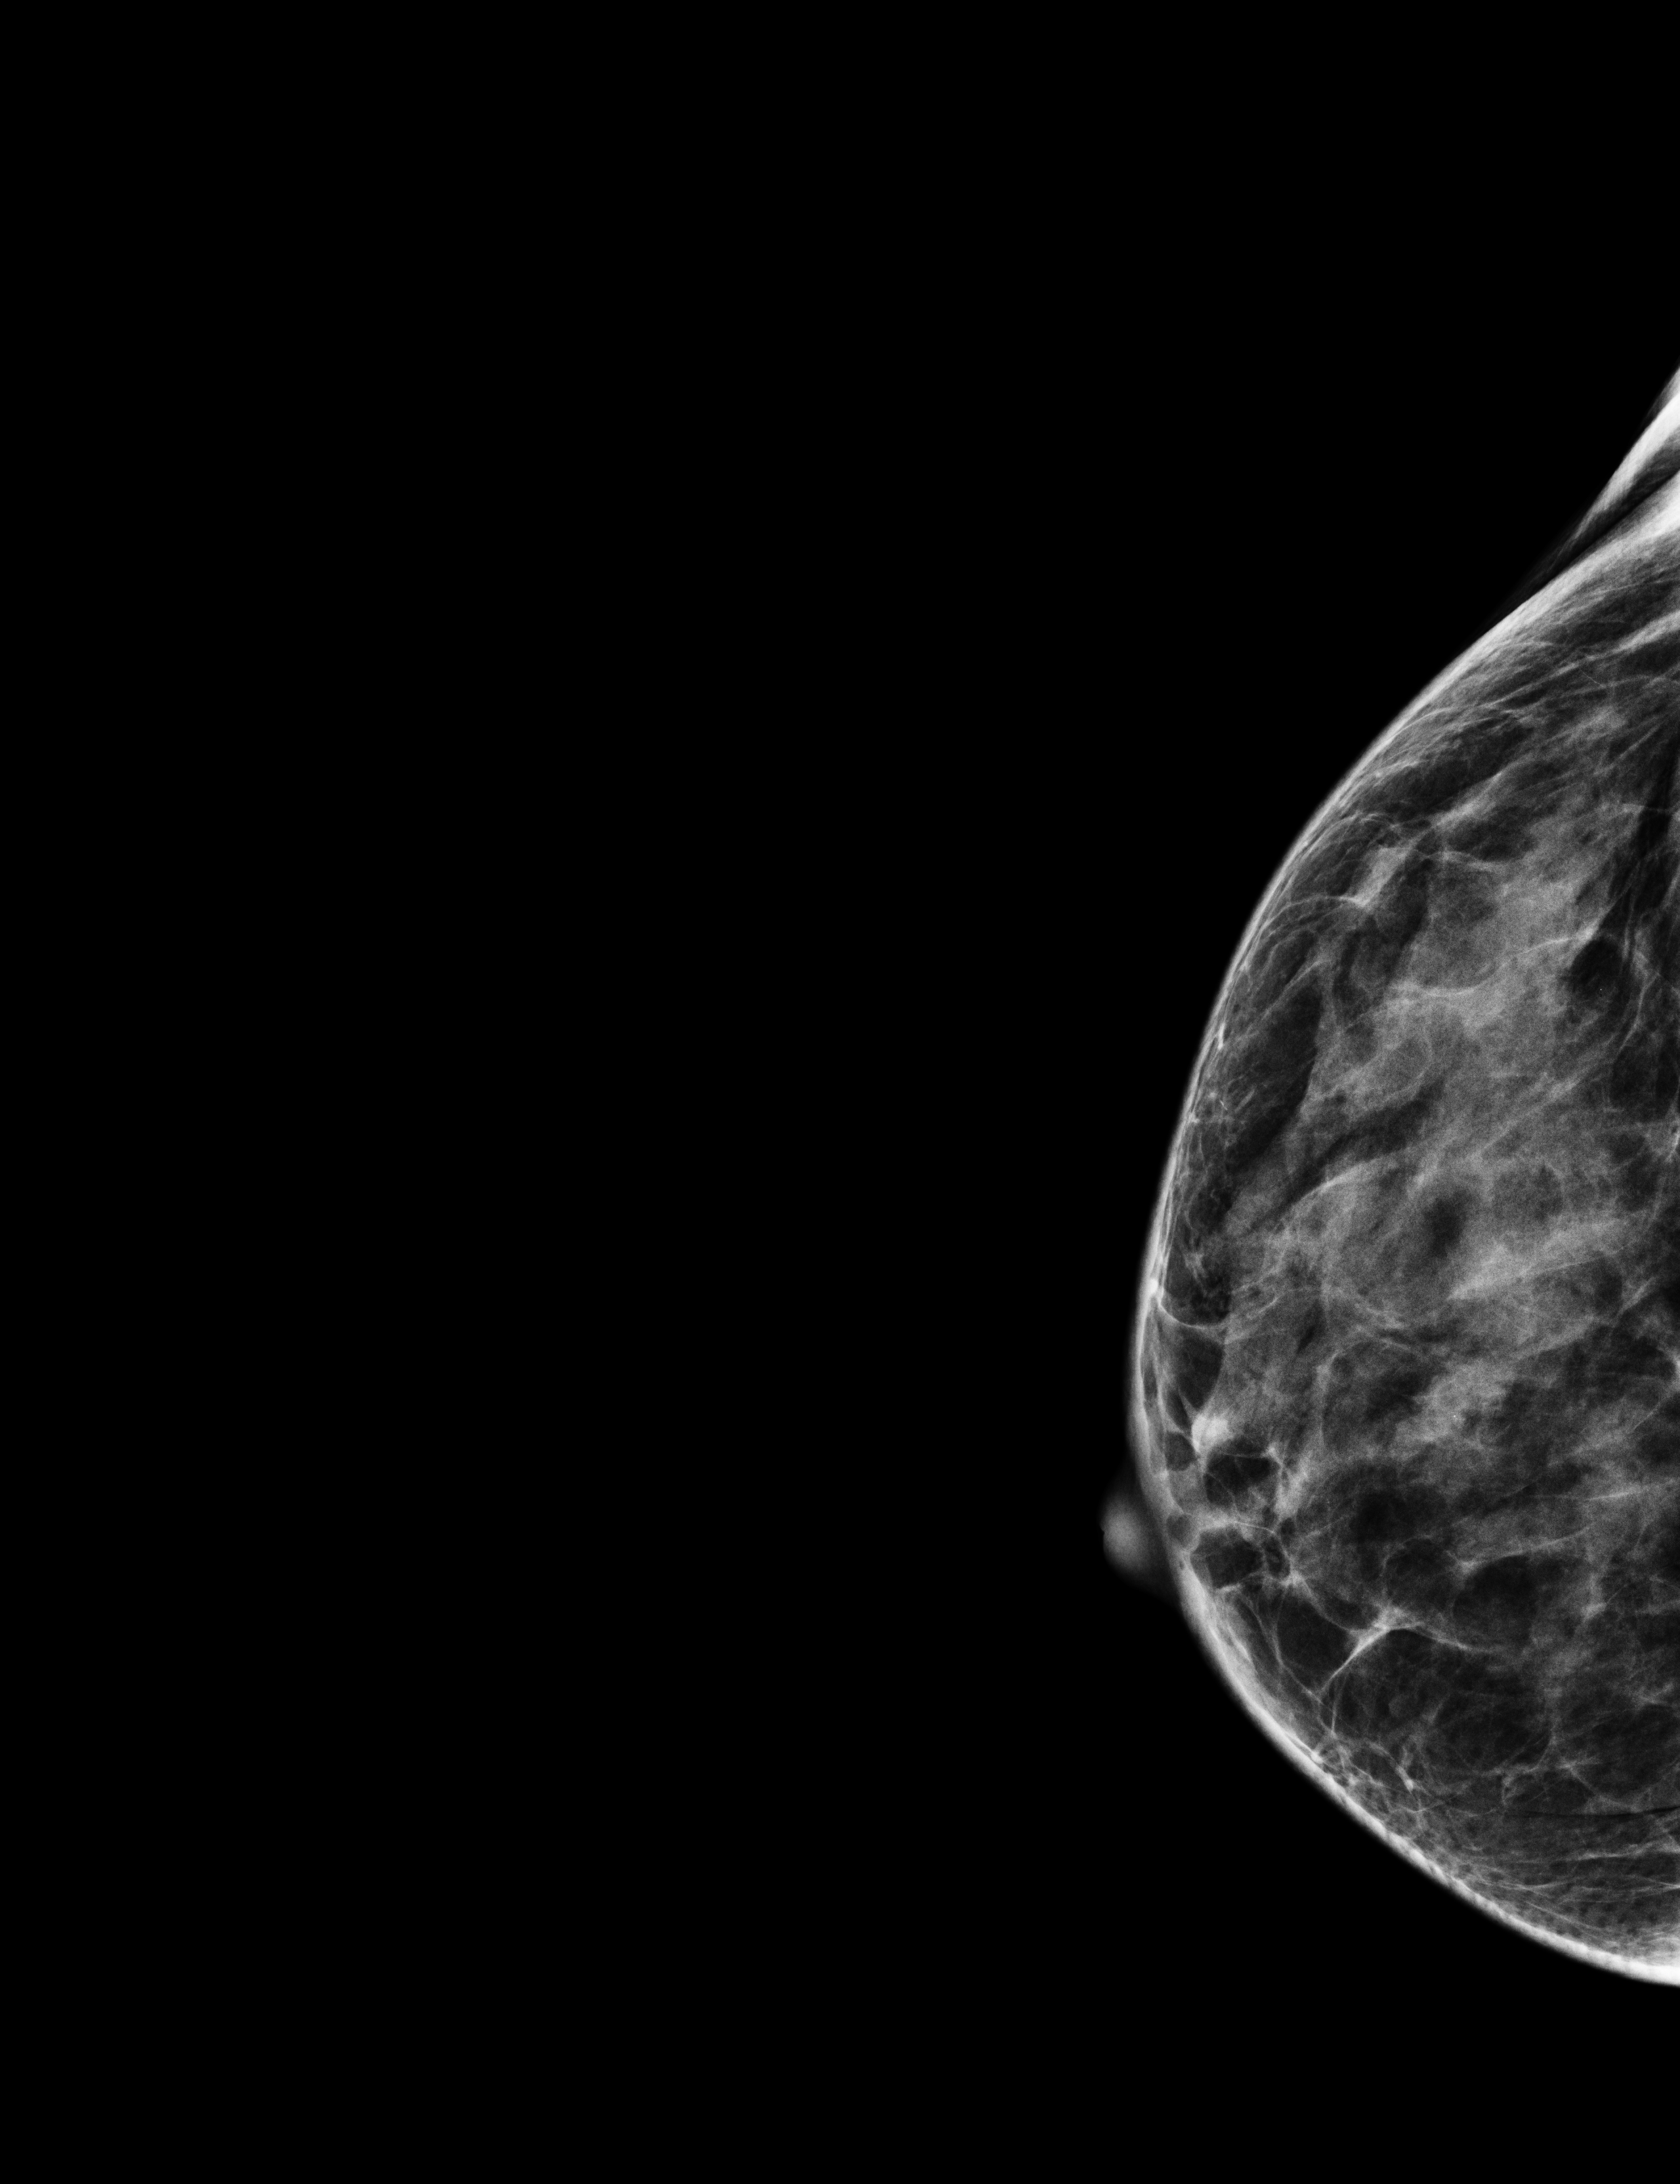
Full-field digital mammogram (FFDM); right breast; exaggerated CC view (lateral); annual screening mammography examination. Patient aged 52 years (female).
- breast density at the screening exam (both breasts): heterogeneously dense (BI-RADS density category c)
- final BI-RADS assessment for this screening round (tomosynthesis exam, both breasts): category 1
- recall: no recall after this screen